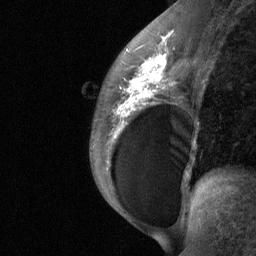
Breast MRI (dynamic contrast-enhanced), one sagittal slice; position 39 of 64 along the scan axis; dynamic contrast-enhanced study with each time point stored as its own series, time point 2 of 3 at this slice position (early post-contrast, ordered by acquisition time); 1.5 T; TE 4.8 ms, TR 27 ms; 2 mm slice thickness; 256 × 256 image matrix, field of view 200 × 200 mm. Female patient, age 34 years. Case-level facts recorded for this patient, not image findings: setting: breast cancer imaged before/during neoadjuvant chemotherapy; receptor status: HR-positive, HER2-negative.
Outlined on this slice (semi-automatically segmented with operator editing):
- analysis volume of interest (the breast-tissue region the enhancement analysis was run in; not a lesion): bounding box (x1, y1, x2, y2) in pixels: (92, 50, 188, 185)
- tumour enhancement mask (voxels above the 90 % enhancement threshold inside the analysis volume of interest): (116, 54, 167, 131)